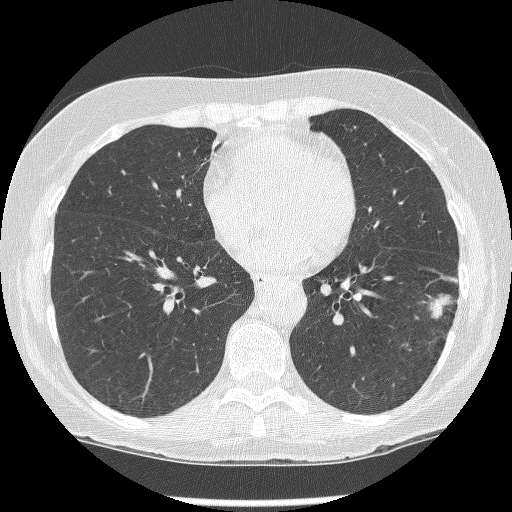
Chest CT (low-dose screening protocol), one axial image; baseline screening round; lung window (W 1500 / L -600 HU); 1.25 mm slice thickness; 512 × 512 image matrix, field of view 303 × 303 mm. Female participant, aged 62 years at enrolment.
Expert reader's lesion annotation, box from (x=414, y=283) to (x=460, y=344) px. The screening reader recorded 2 non-calcified nodules or masses ≥4 mm on this exam; which of them this box marks is not recorded. Official screen result: positive, change unspecified: nodule(s) >= 4 mm or enlarging nodule(s), mass(es), or other non-specific abnormalities suspicious for lung cancer. Participant outcome: lung cancer diagnosed 15 days after this screen — non-small cell carcinoma, left lower lobe, stage IIIB (AJCC 6th edition), 23 mm at pathology.